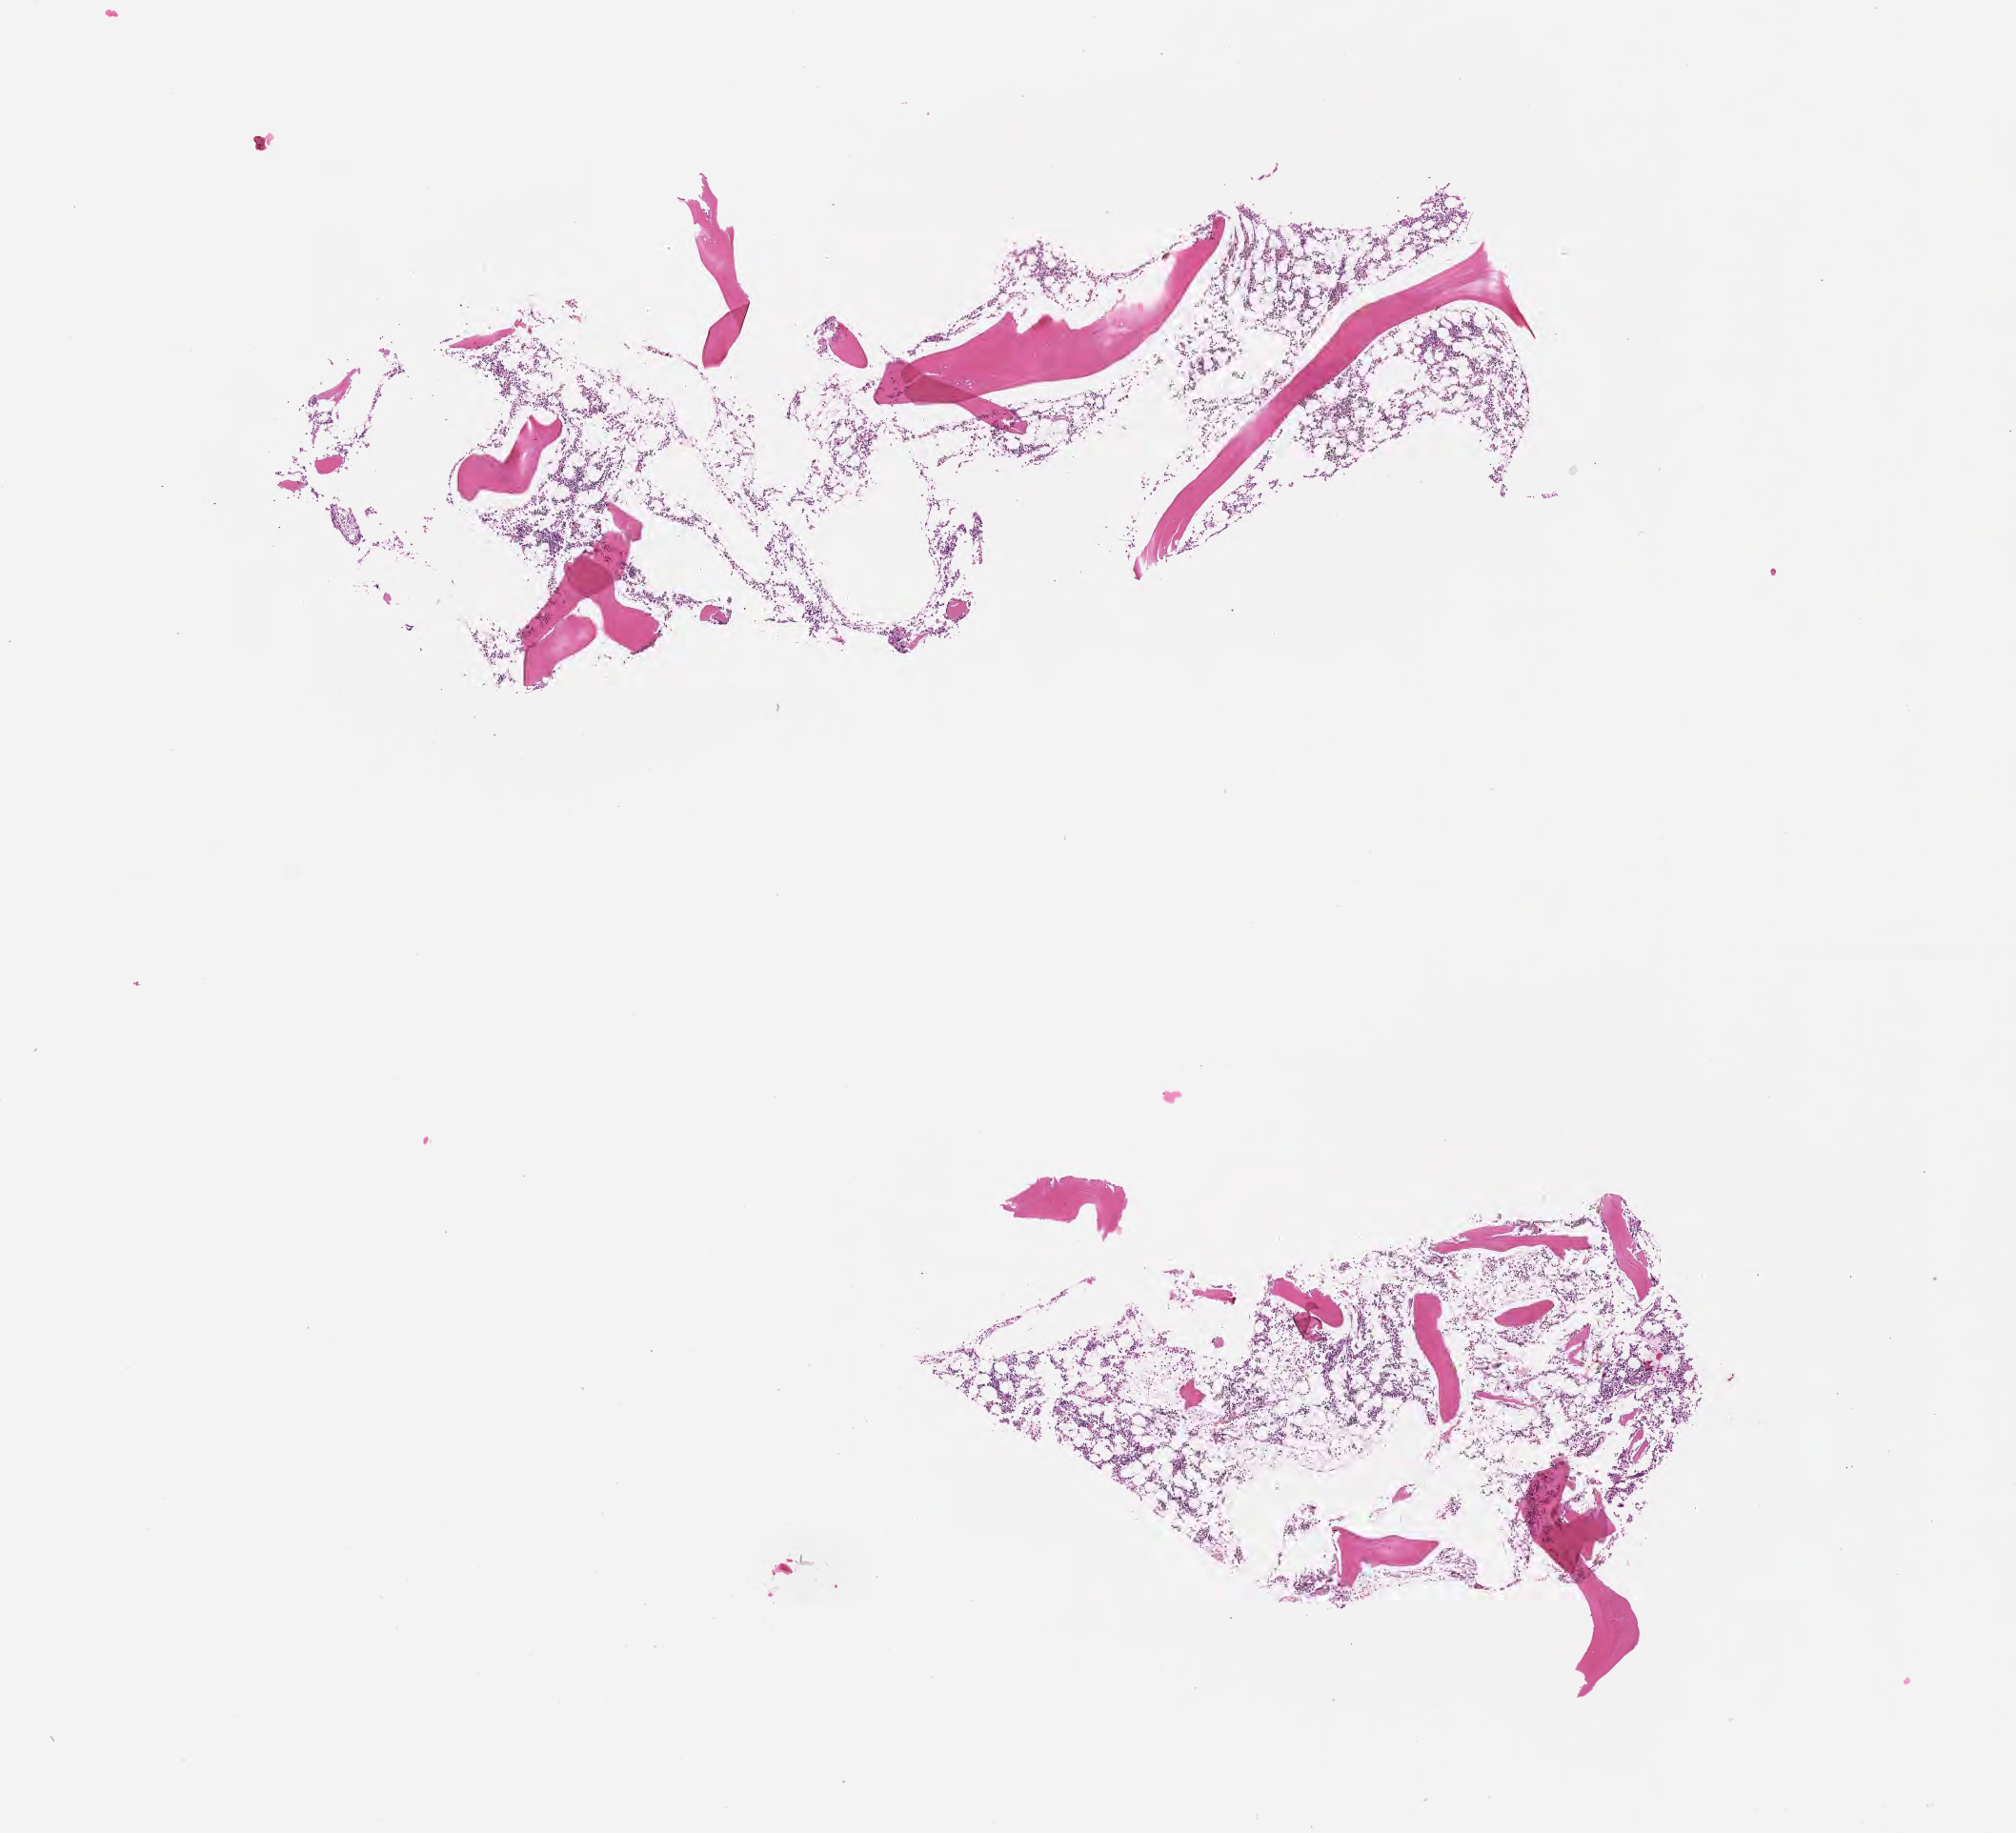
Whole-slide image, hematoxylin and eosin (H&E) stain — shown as a low-resolution overview of the whole scanned area (about 8.6 x 7.8 mm), formalin-fixed paraffin-embedded section, specimen: non-tumor (normal tissue) sample from a patient with burkitt lymphoma, NOS. Patient: male, age at initial diagnosis 9 years. Slide review estimates, as recorded: tumor cells 0%, tumor nuclei 0%, stromal cells 0%, necrosis 0%, normal cells 100%. Infiltration values recorded for this section: lymphocyte infiltration 10%, monocyte infiltration 10%, neutrophil infiltration 50%.
• this section: non-tumor tissue sample; the patient's diagnosis is given above
• section: bottom of the tissue portion